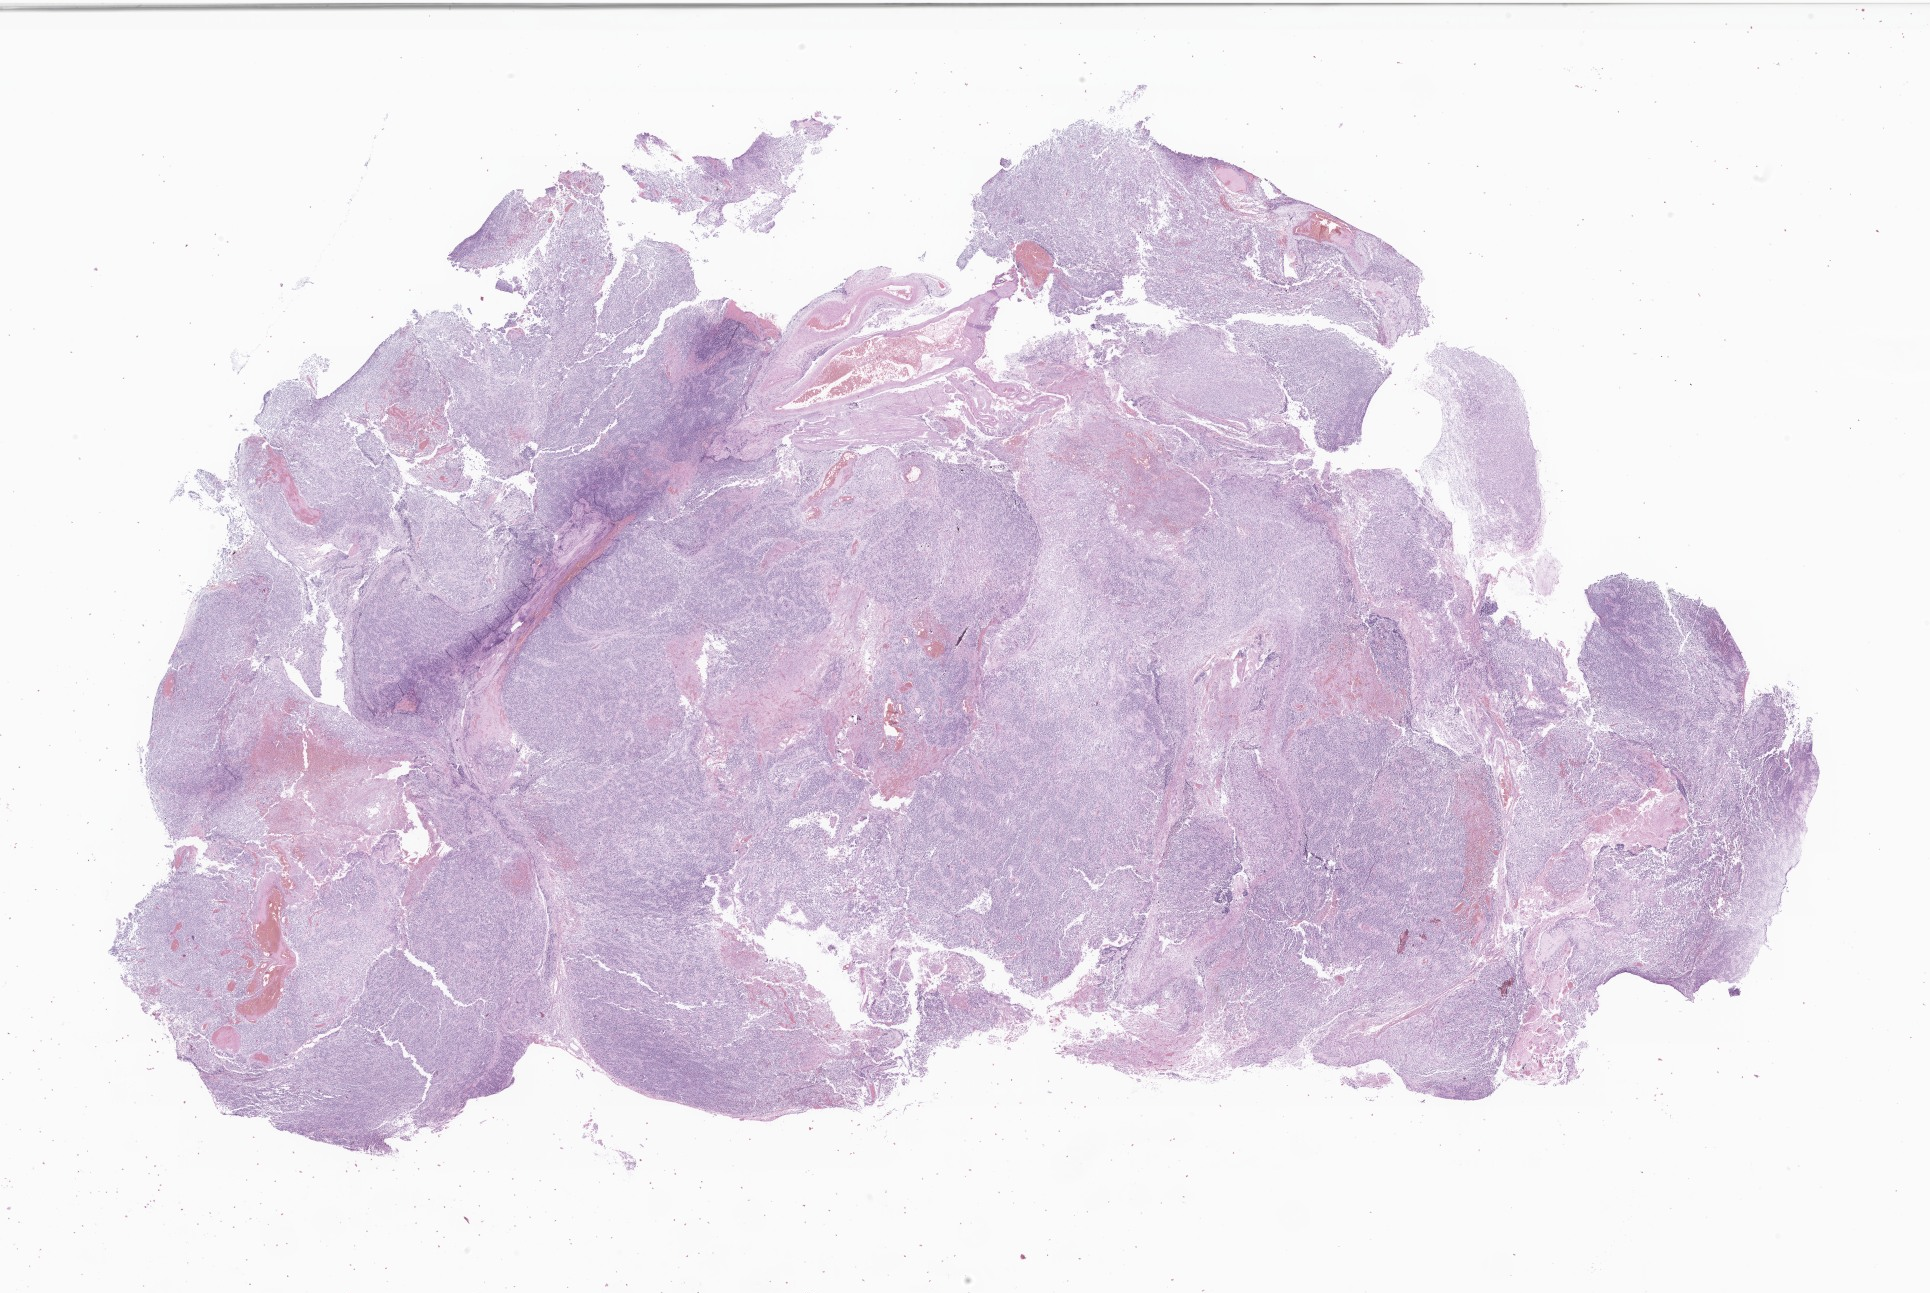
Hematoxylin and eosin (H&E) whole-slide image of tumor tissue from the brain — whole scanned area (about 32.5 x 21.8 mm) shown as a low-resolution overview, FFPE section. Patient: male, age 174 months (14 years 6 months).
Recorded diagnosis: Ependymoma, NOS.